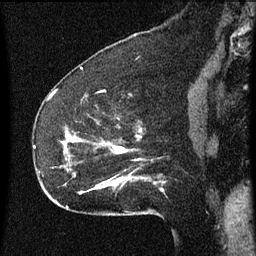
Breast MRI (dynamic contrast-enhanced), one sagittal slice. Slice 21 of 60 in the series (ordered by position). Dynamic contrast-enhanced series, image 2 of 3 at this slice position (ordered by acquisition). 1.5 T. TE 4.2 ms, TR 8 ms. 2 mm slice thickness. 256 × 256 image matrix. Patient: female, 52 years.
Annotated regions visible in this slice (semi-automatically segmented with operator editing):
- analysis volume of interest (the breast-tissue region the enhancement analysis was run in; not a lesion): bounding box <54,110,164,207> (left, top, right, bottom; pixels)
- tumour enhancement mask (voxels above the 70 % enhancement threshold inside the analysis volume of interest): <65,138,164,191>